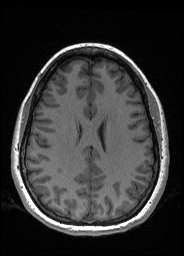
Pre-operative brain MRI before brain-tumour surgery, one axial slice. Slice 72 of 176 in the series (ordered by position). T1-weighted post-contrast. 184 × 256 image matrix, field of view 180 × 250 mm. Case-level facts recorded for this patient, not image findings: histopathology: Oligodendroglioma; WHO grade: 2; IDH mutation: yes; tumour location: Left Frontal.
Structures marked on this image (manually delineated by an expert):
- tumour: bounding box (x1, y1, x2, y2) in pixels: (100, 112, 106, 121)